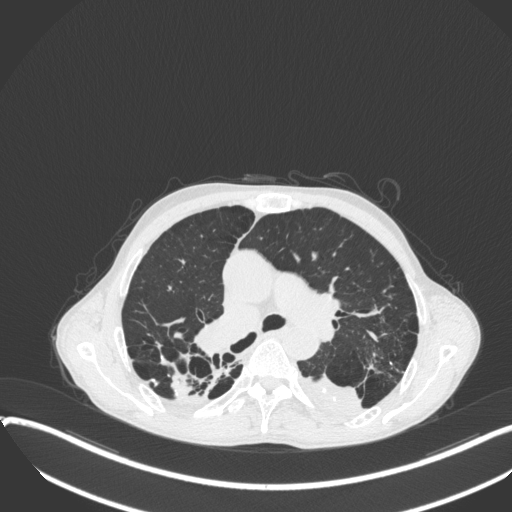
Chest CT, one axial slice. Position 245 of 400 along the scan axis. Reconstruction kernel B31f. Lung window (W 1500 / L -600 HU). 1 mm slice thickness. 512 × 512 image matrix, field of view 400 × 400 mm. Male patient, age 57 years. From the clinical record (not read from this slice): clinical TNM (as recorded): T4 N0 M0.
Outlined on this slice (rectangle marked by the reading radiologist):
- lung tumour (recorded histology: squamous cell carcinoma): bounding box (x1, y1, x2, y2) in pixels: (298, 366, 365, 424)